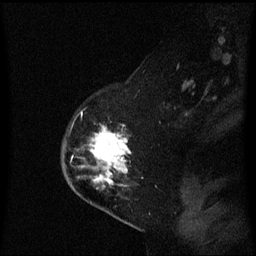
Breast MRI (dynamic contrast-enhanced), one sagittal slice; slice 44 of 60 in the series (ordered by position); dynamic contrast-enhanced series, image 2 of 3 at this slice position (ordered by acquisition); 1.5 T; TE 4.2 ms, TR 8.4 ms; 2 mm slice thickness; 256 × 256 image matrix, field of view 210 × 210 mm. Patient: female, 54 years. Case-level facts recorded for this patient, not image findings: setting: breast cancer imaged before/during neoadjuvant chemotherapy; receptor status: HER2-positive.
Outlined on this slice (semi-automatic segmentation, software-assisted and operator-edited):
- analysis volume of interest (the breast-tissue region the enhancement analysis was run in; not a lesion): bounding box (x1, y1, x2, y2) in pixels: (64, 130, 140, 198)
- tumour enhancement mask (voxels above the 70 % enhancement threshold inside the analysis volume of interest): (94, 131, 132, 184)